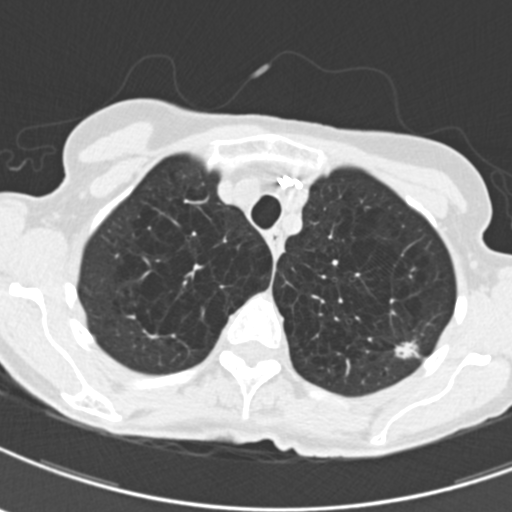
Low-dose screening chest CT, one axial slice; position 163 of 203 along the scan axis; lung window (W 1500 / L -600 HU); 2 mm slice thickness; 512 × 512 image matrix.
Annotated regions visible in this slice (outlined manually by an expert reader):
- lesion 1 (tumor, upper lobe of left lung): bounding box <394,341,420,360> (left, top, right, bottom; pixels)